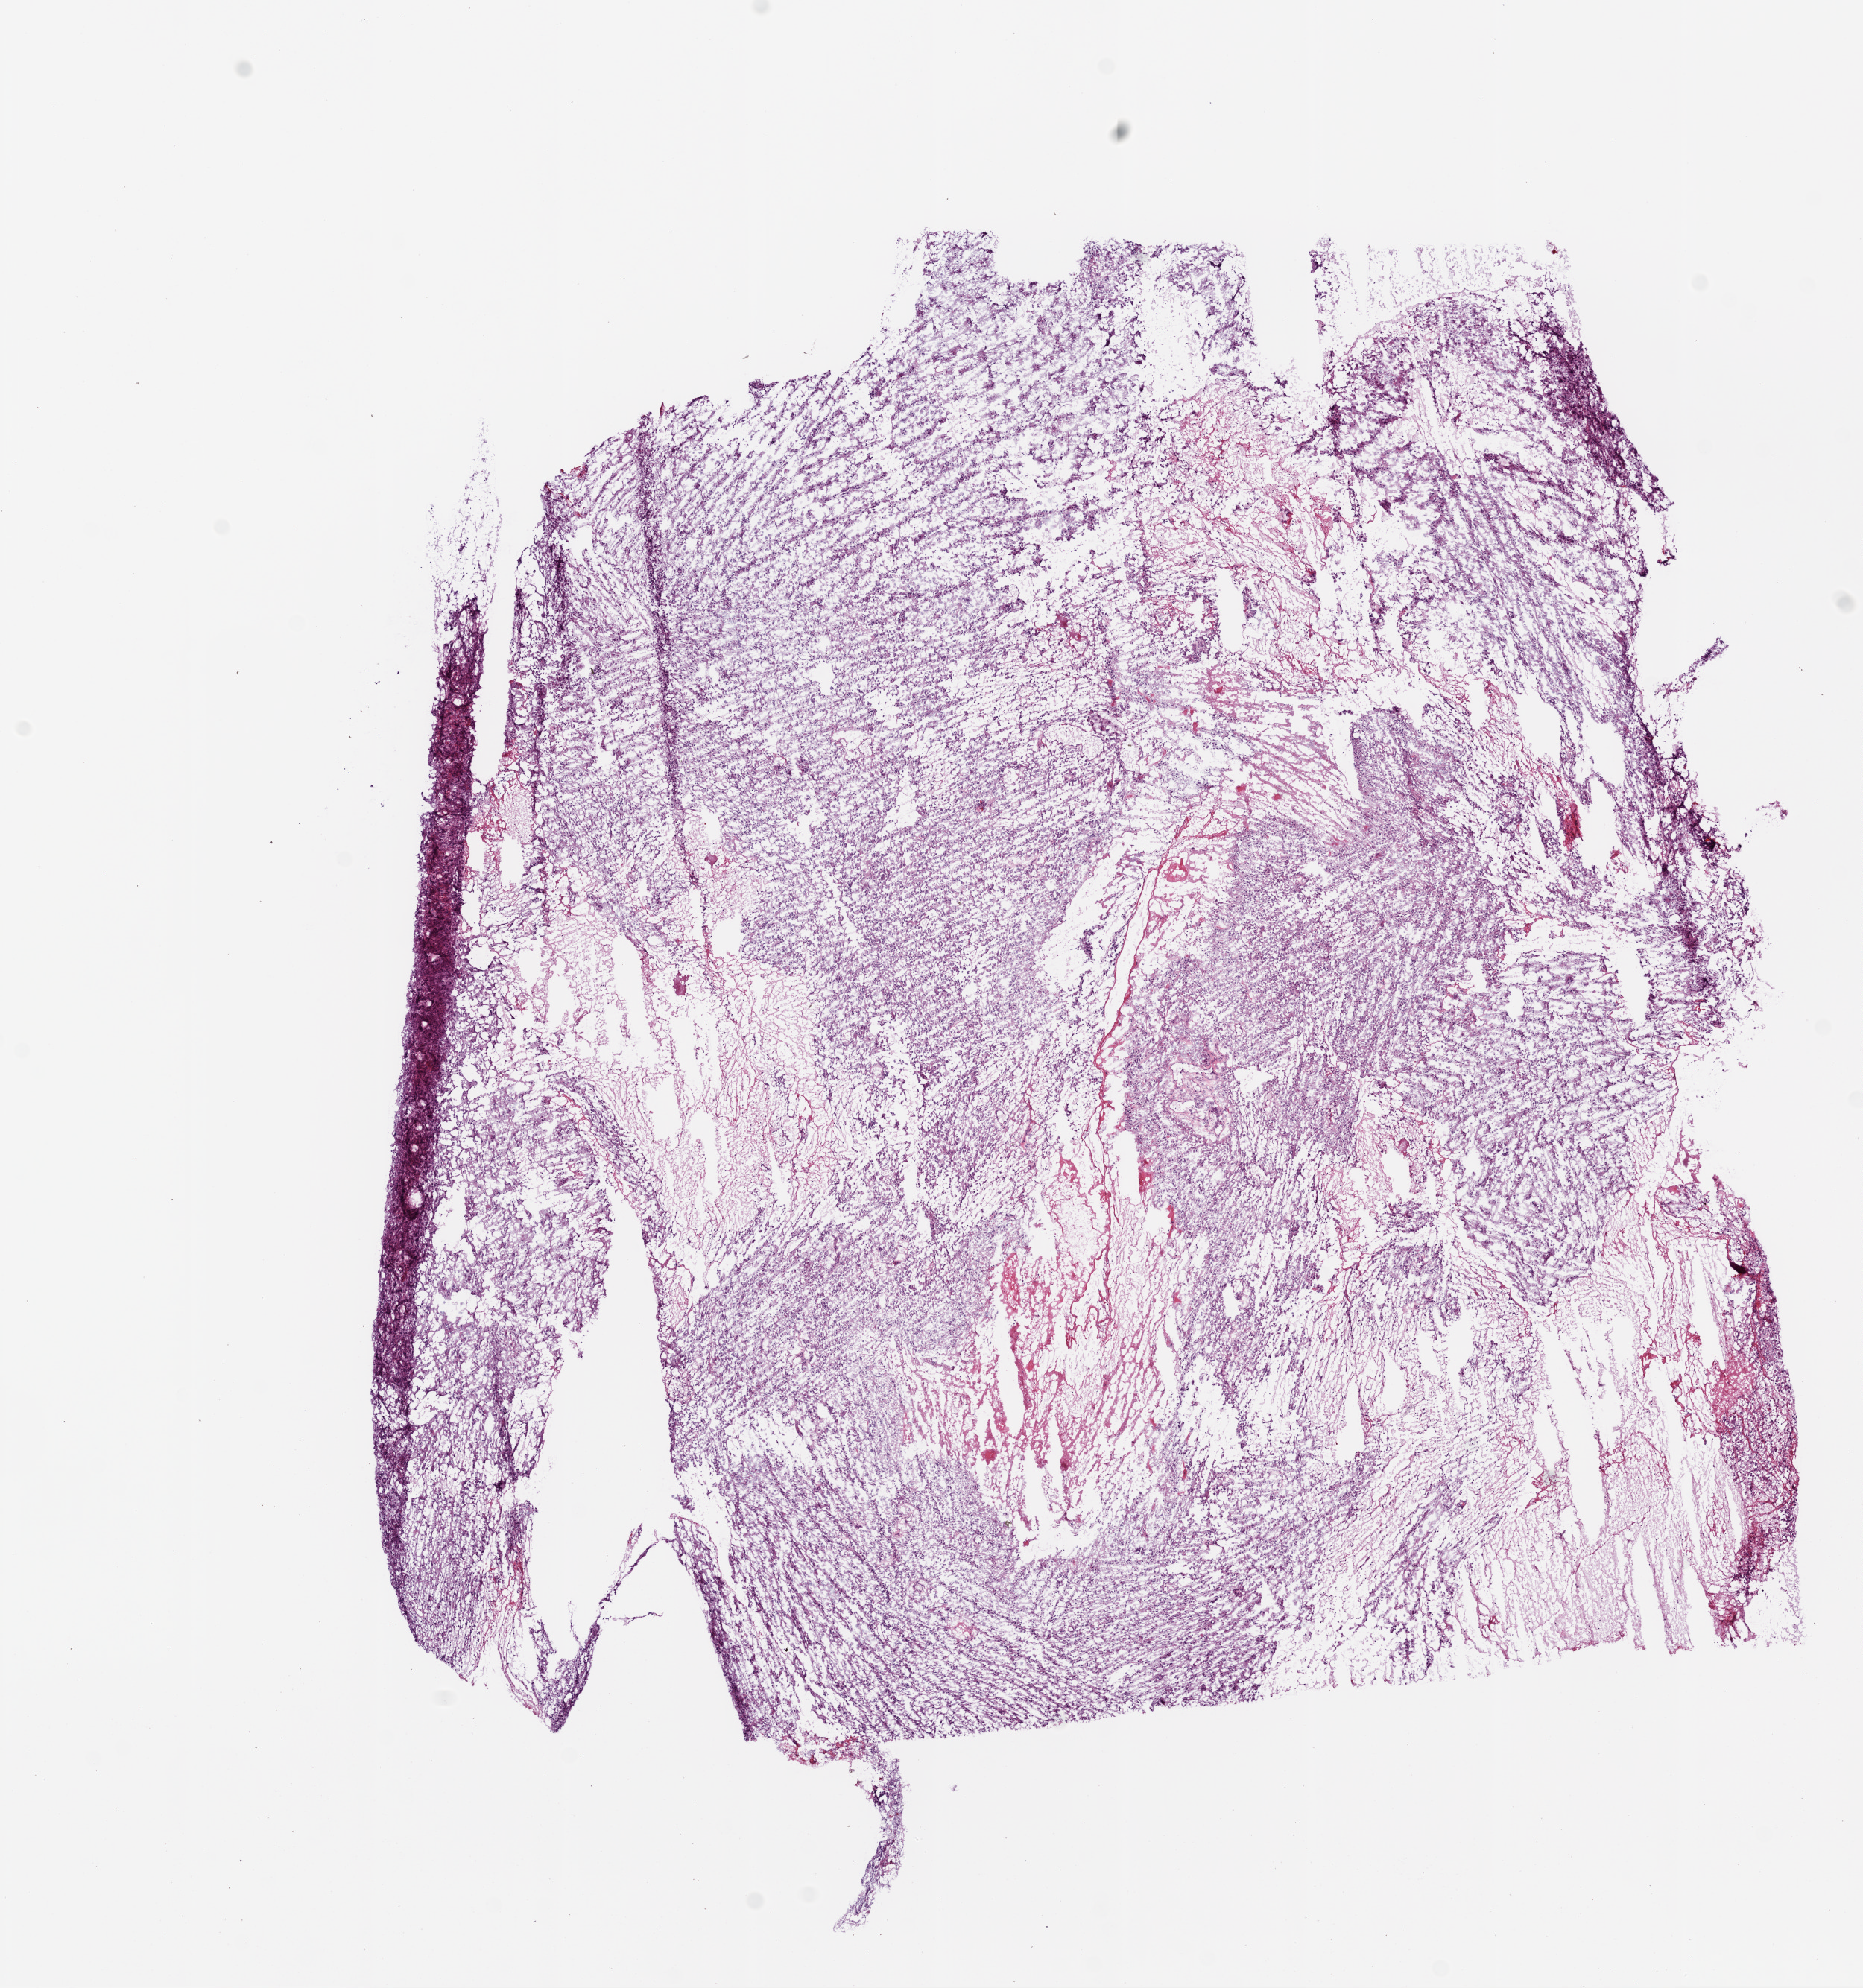
Whole-slide histology image, Hematoxylin and eosin (H&E) stained, a low-resolution overview of the entire scanned area, about 10.0 x 10.7 mm (acquisition: 20x scan), frozen section from the top of the tissue portion, primary tumour sample from the brain. Male, age 65 years at initial diagnosis. Slide review estimates, as recorded: tumour cells 70%, tumour nuclei 80%, normal cells 0%, stromal cells 0%, necrosis 30%.
Pathologic diagnosis: Glioblastoma.